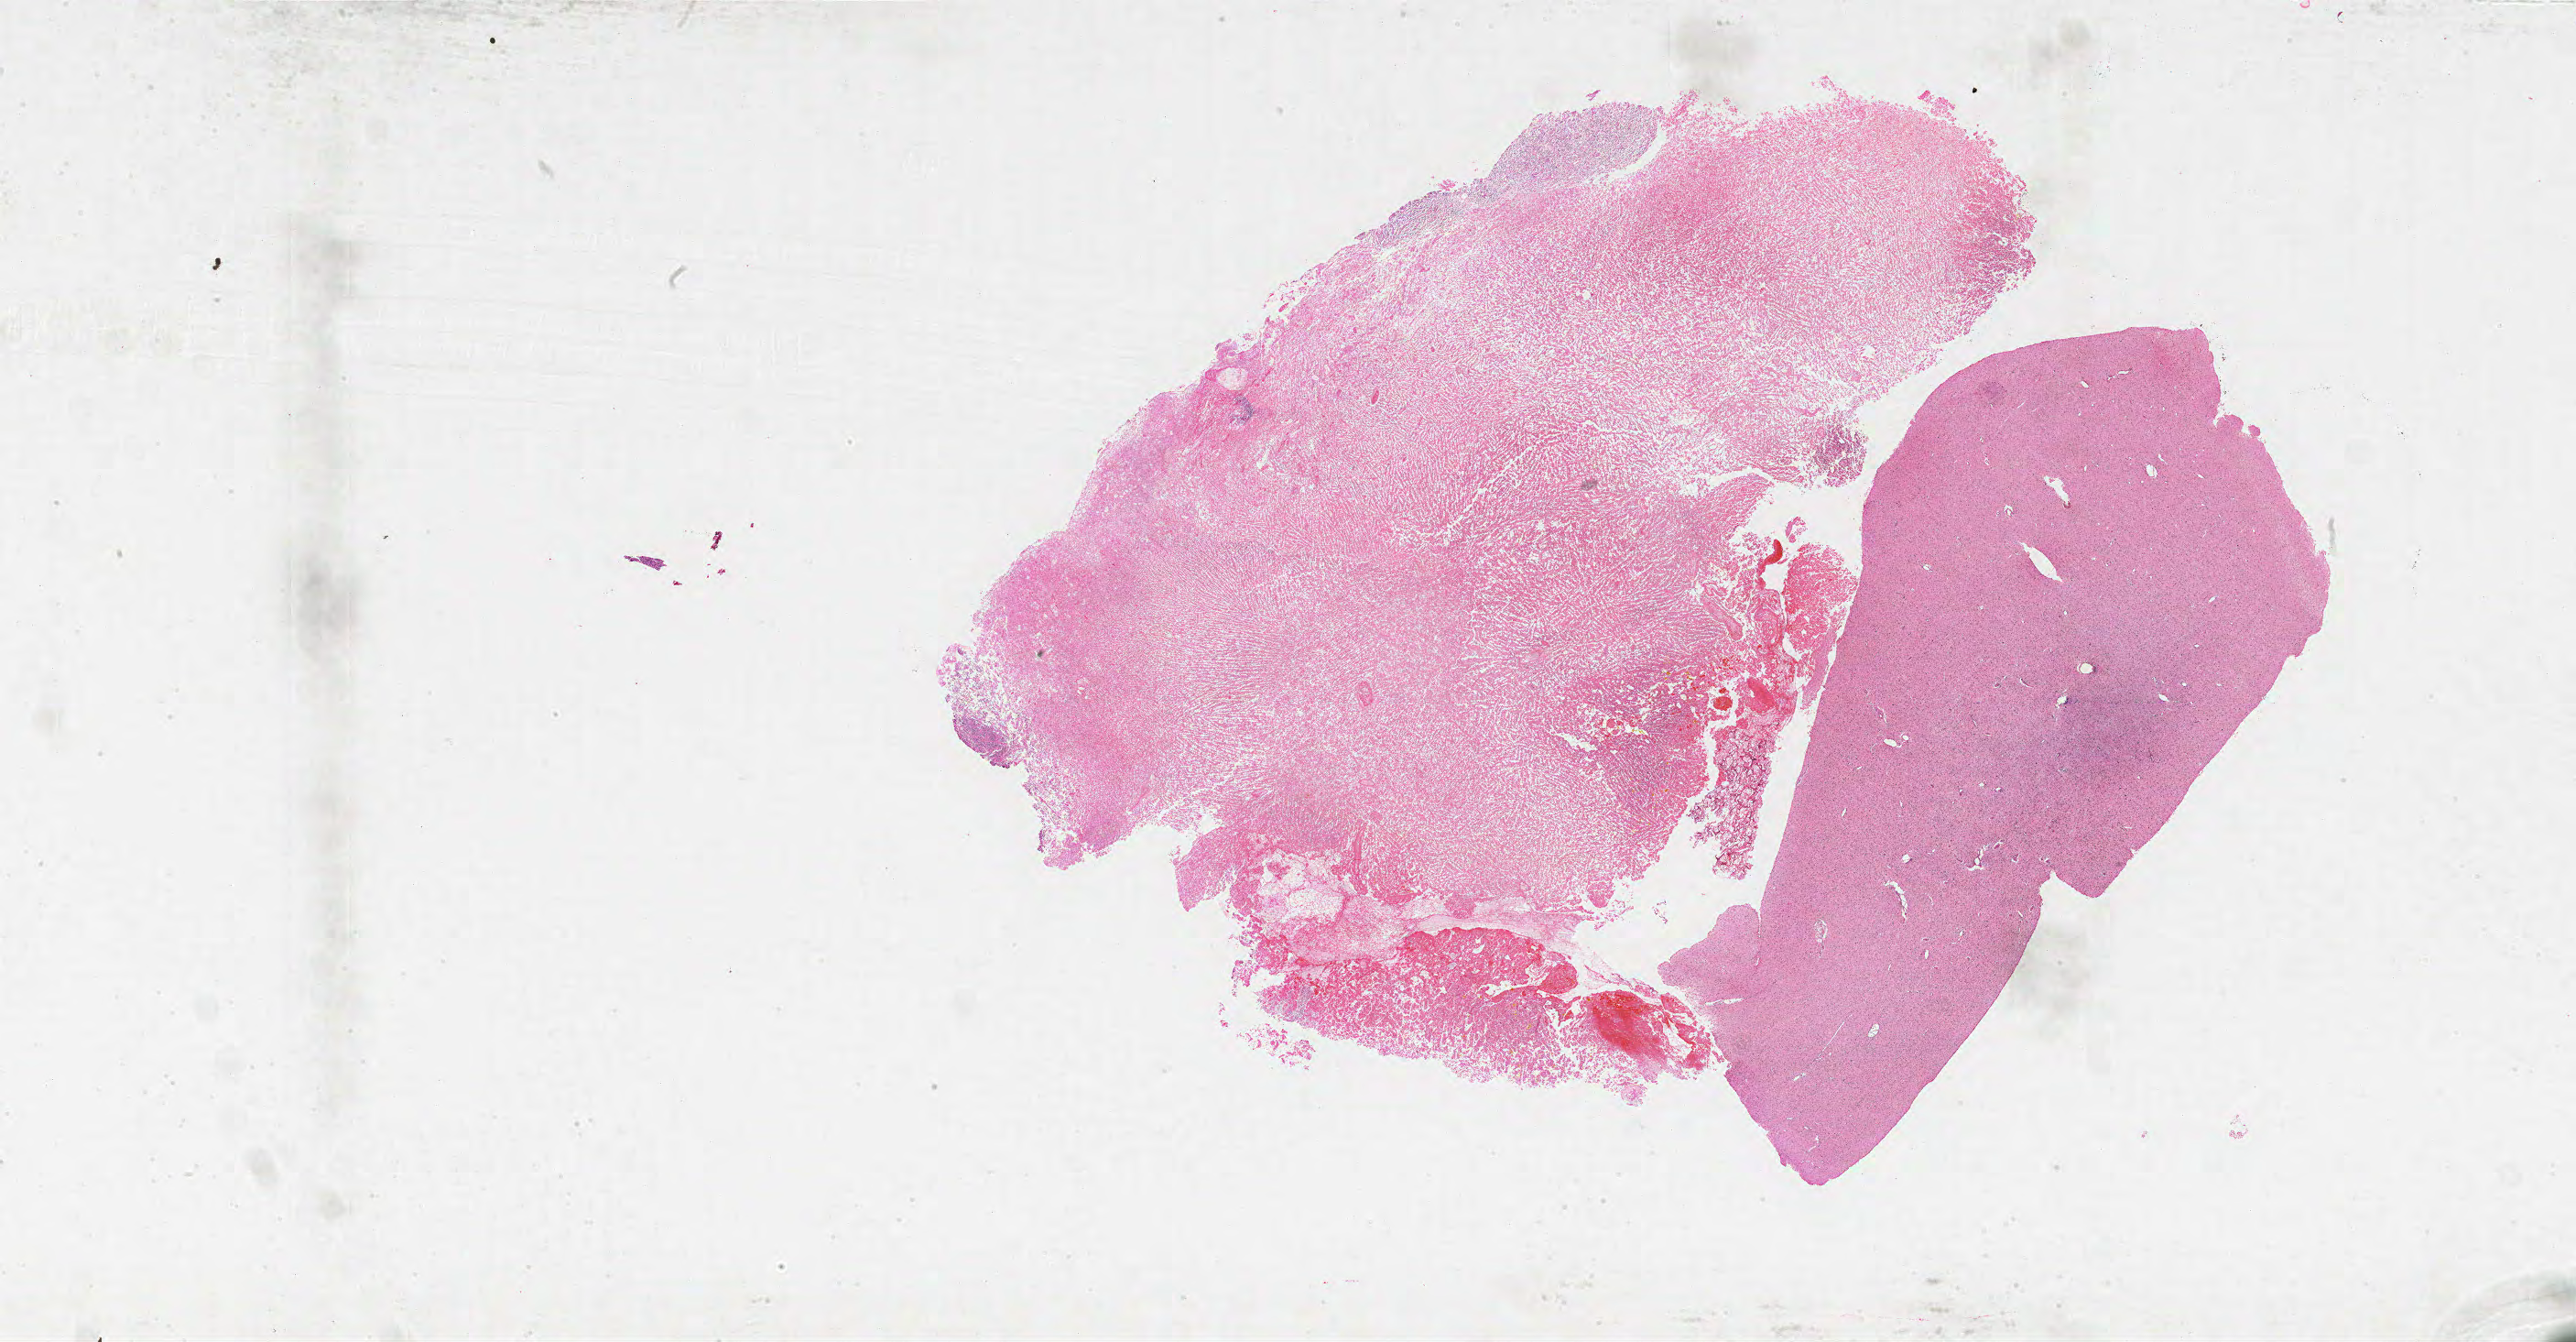
Whole-slide histology image, H&E-stained, shown as a low-resolution overview of the whole scanned area (about 45.0 x 23.4 mm), formalin-fixed paraffin-embedded (FFPE) diagnostic section, brain, primary tumour sample. Female, age 38 years at initial diagnosis.
* diagnosis: Glioblastoma